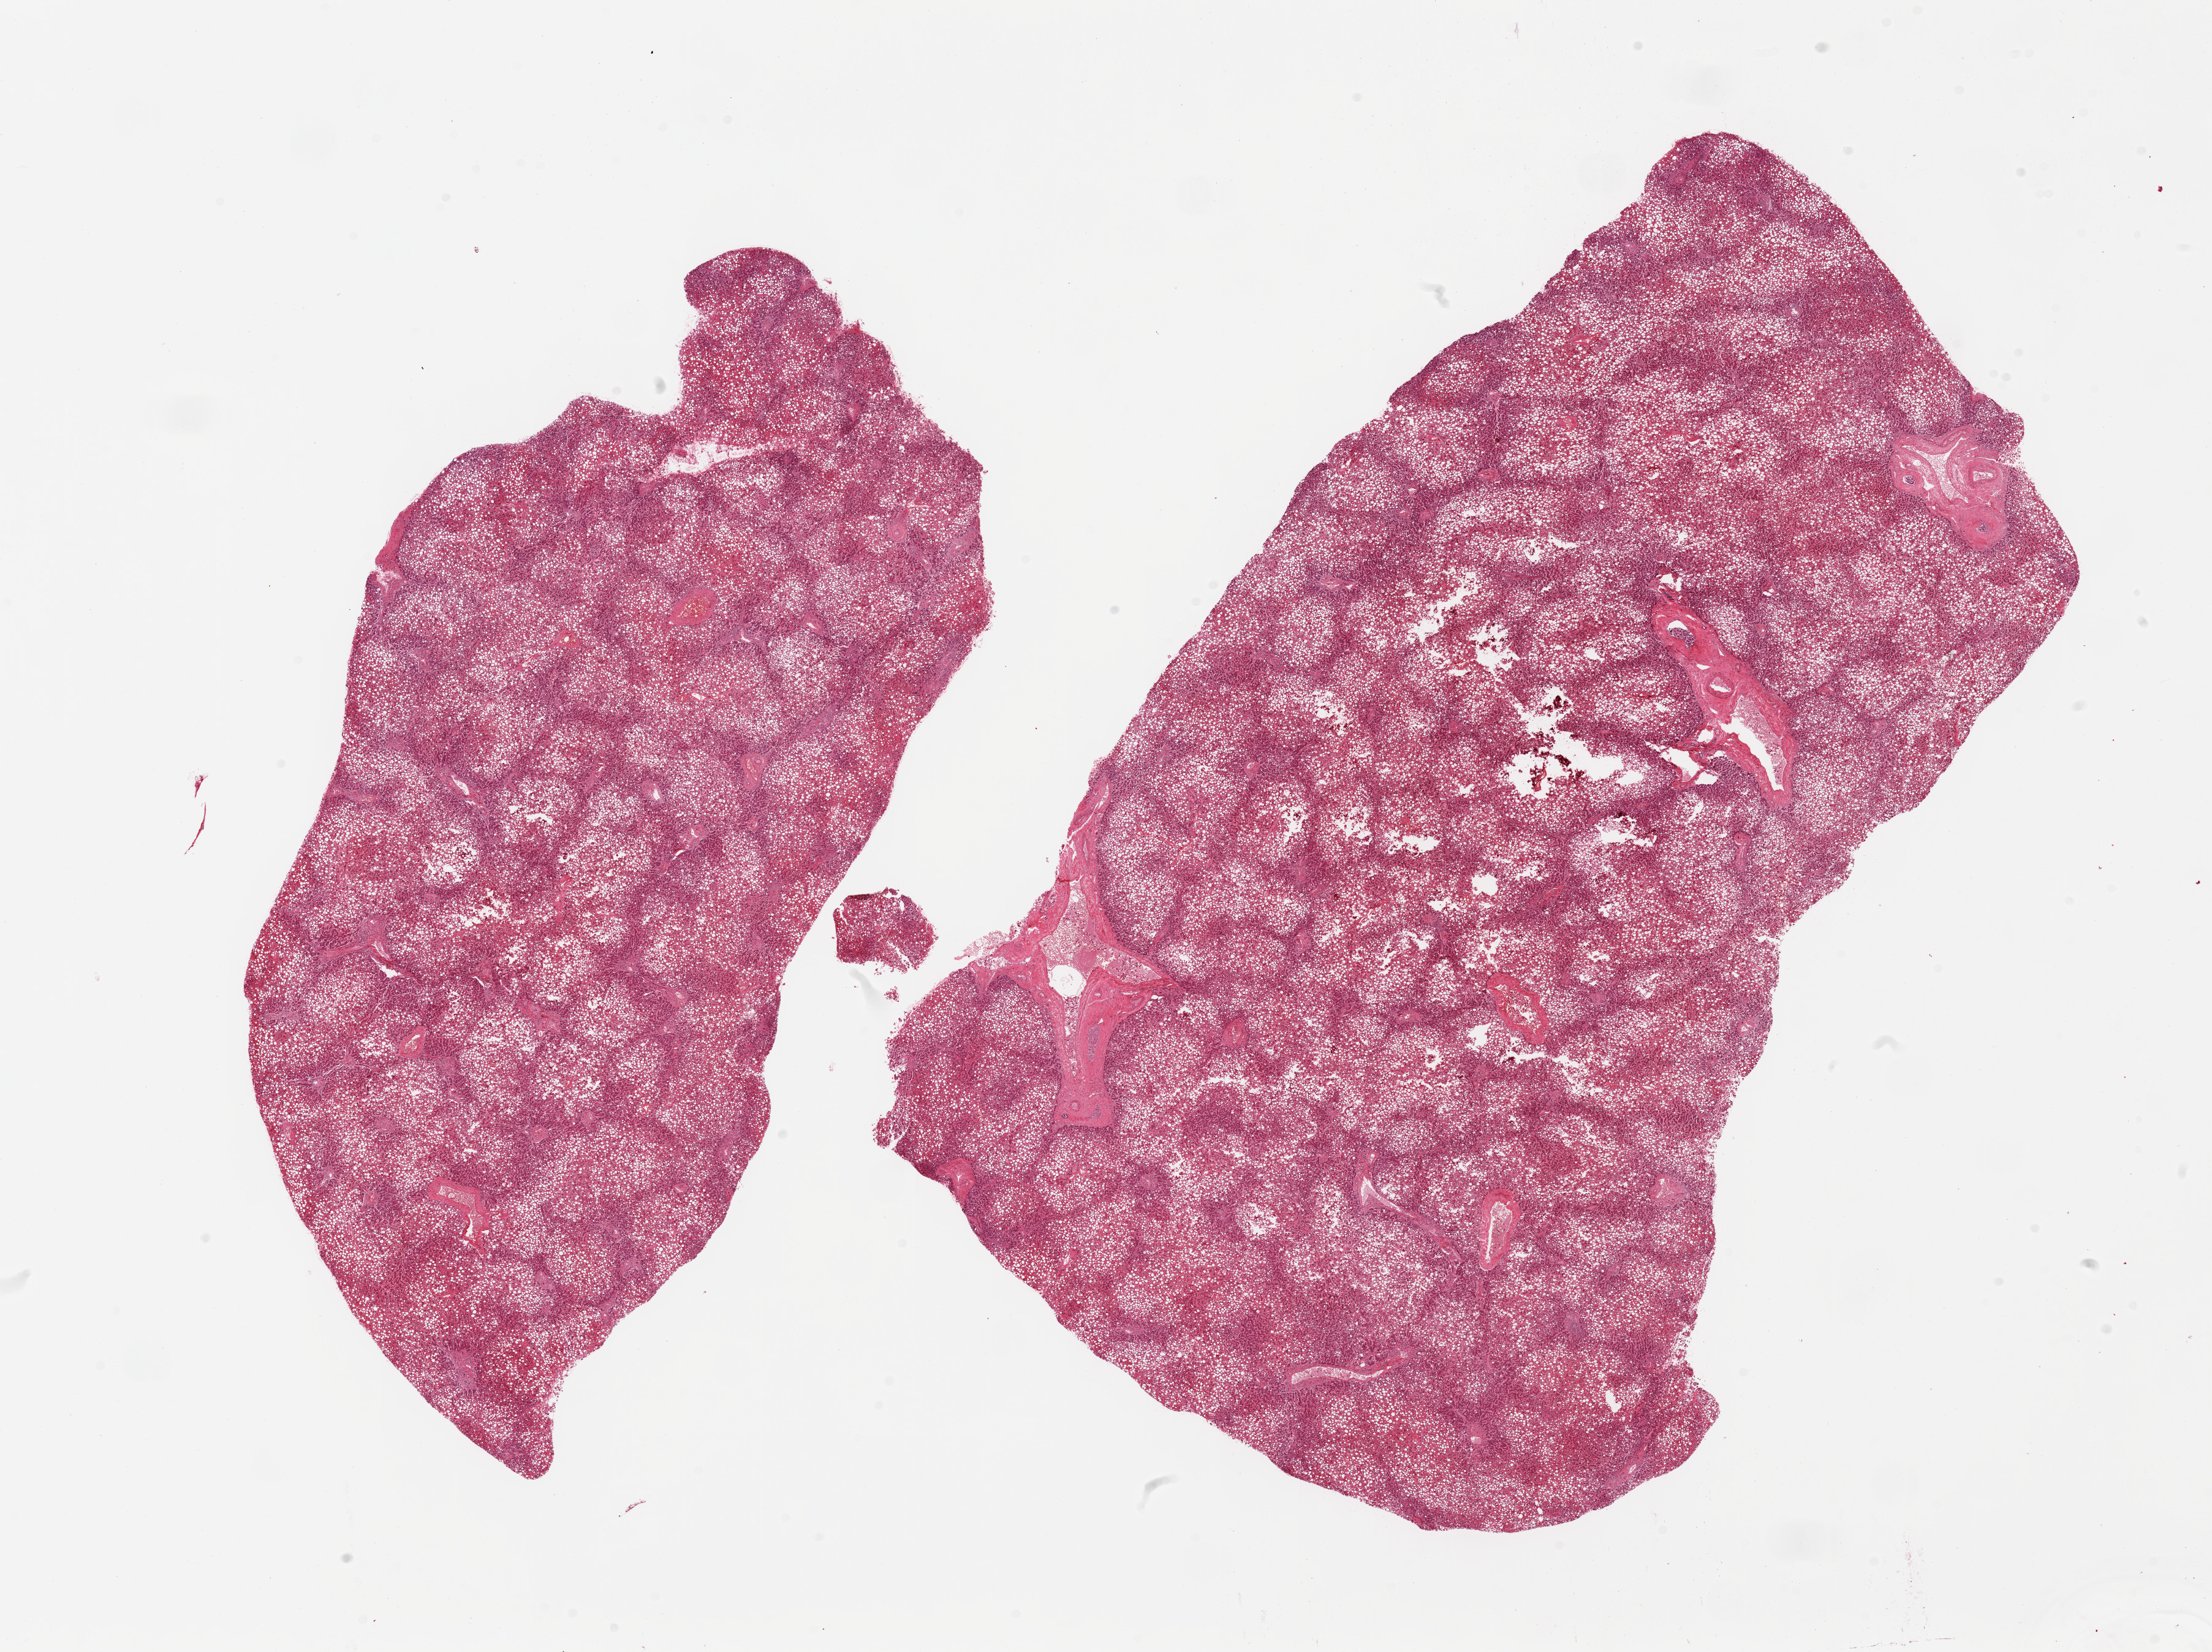
Whole-slide image, H&E stain, brightfield, shown as a low-resolution overview of the whole scanned area (about 28.5 x 21.3 mm, from a 20x scan). PAXgene-fixed, paraffin-embedded tissue. Target tissue: liver. Donor tissue sample. Donor: male.
Review note (as recorded): 2 pieces; severe macrovesicular steatosis; no cirrhosis.